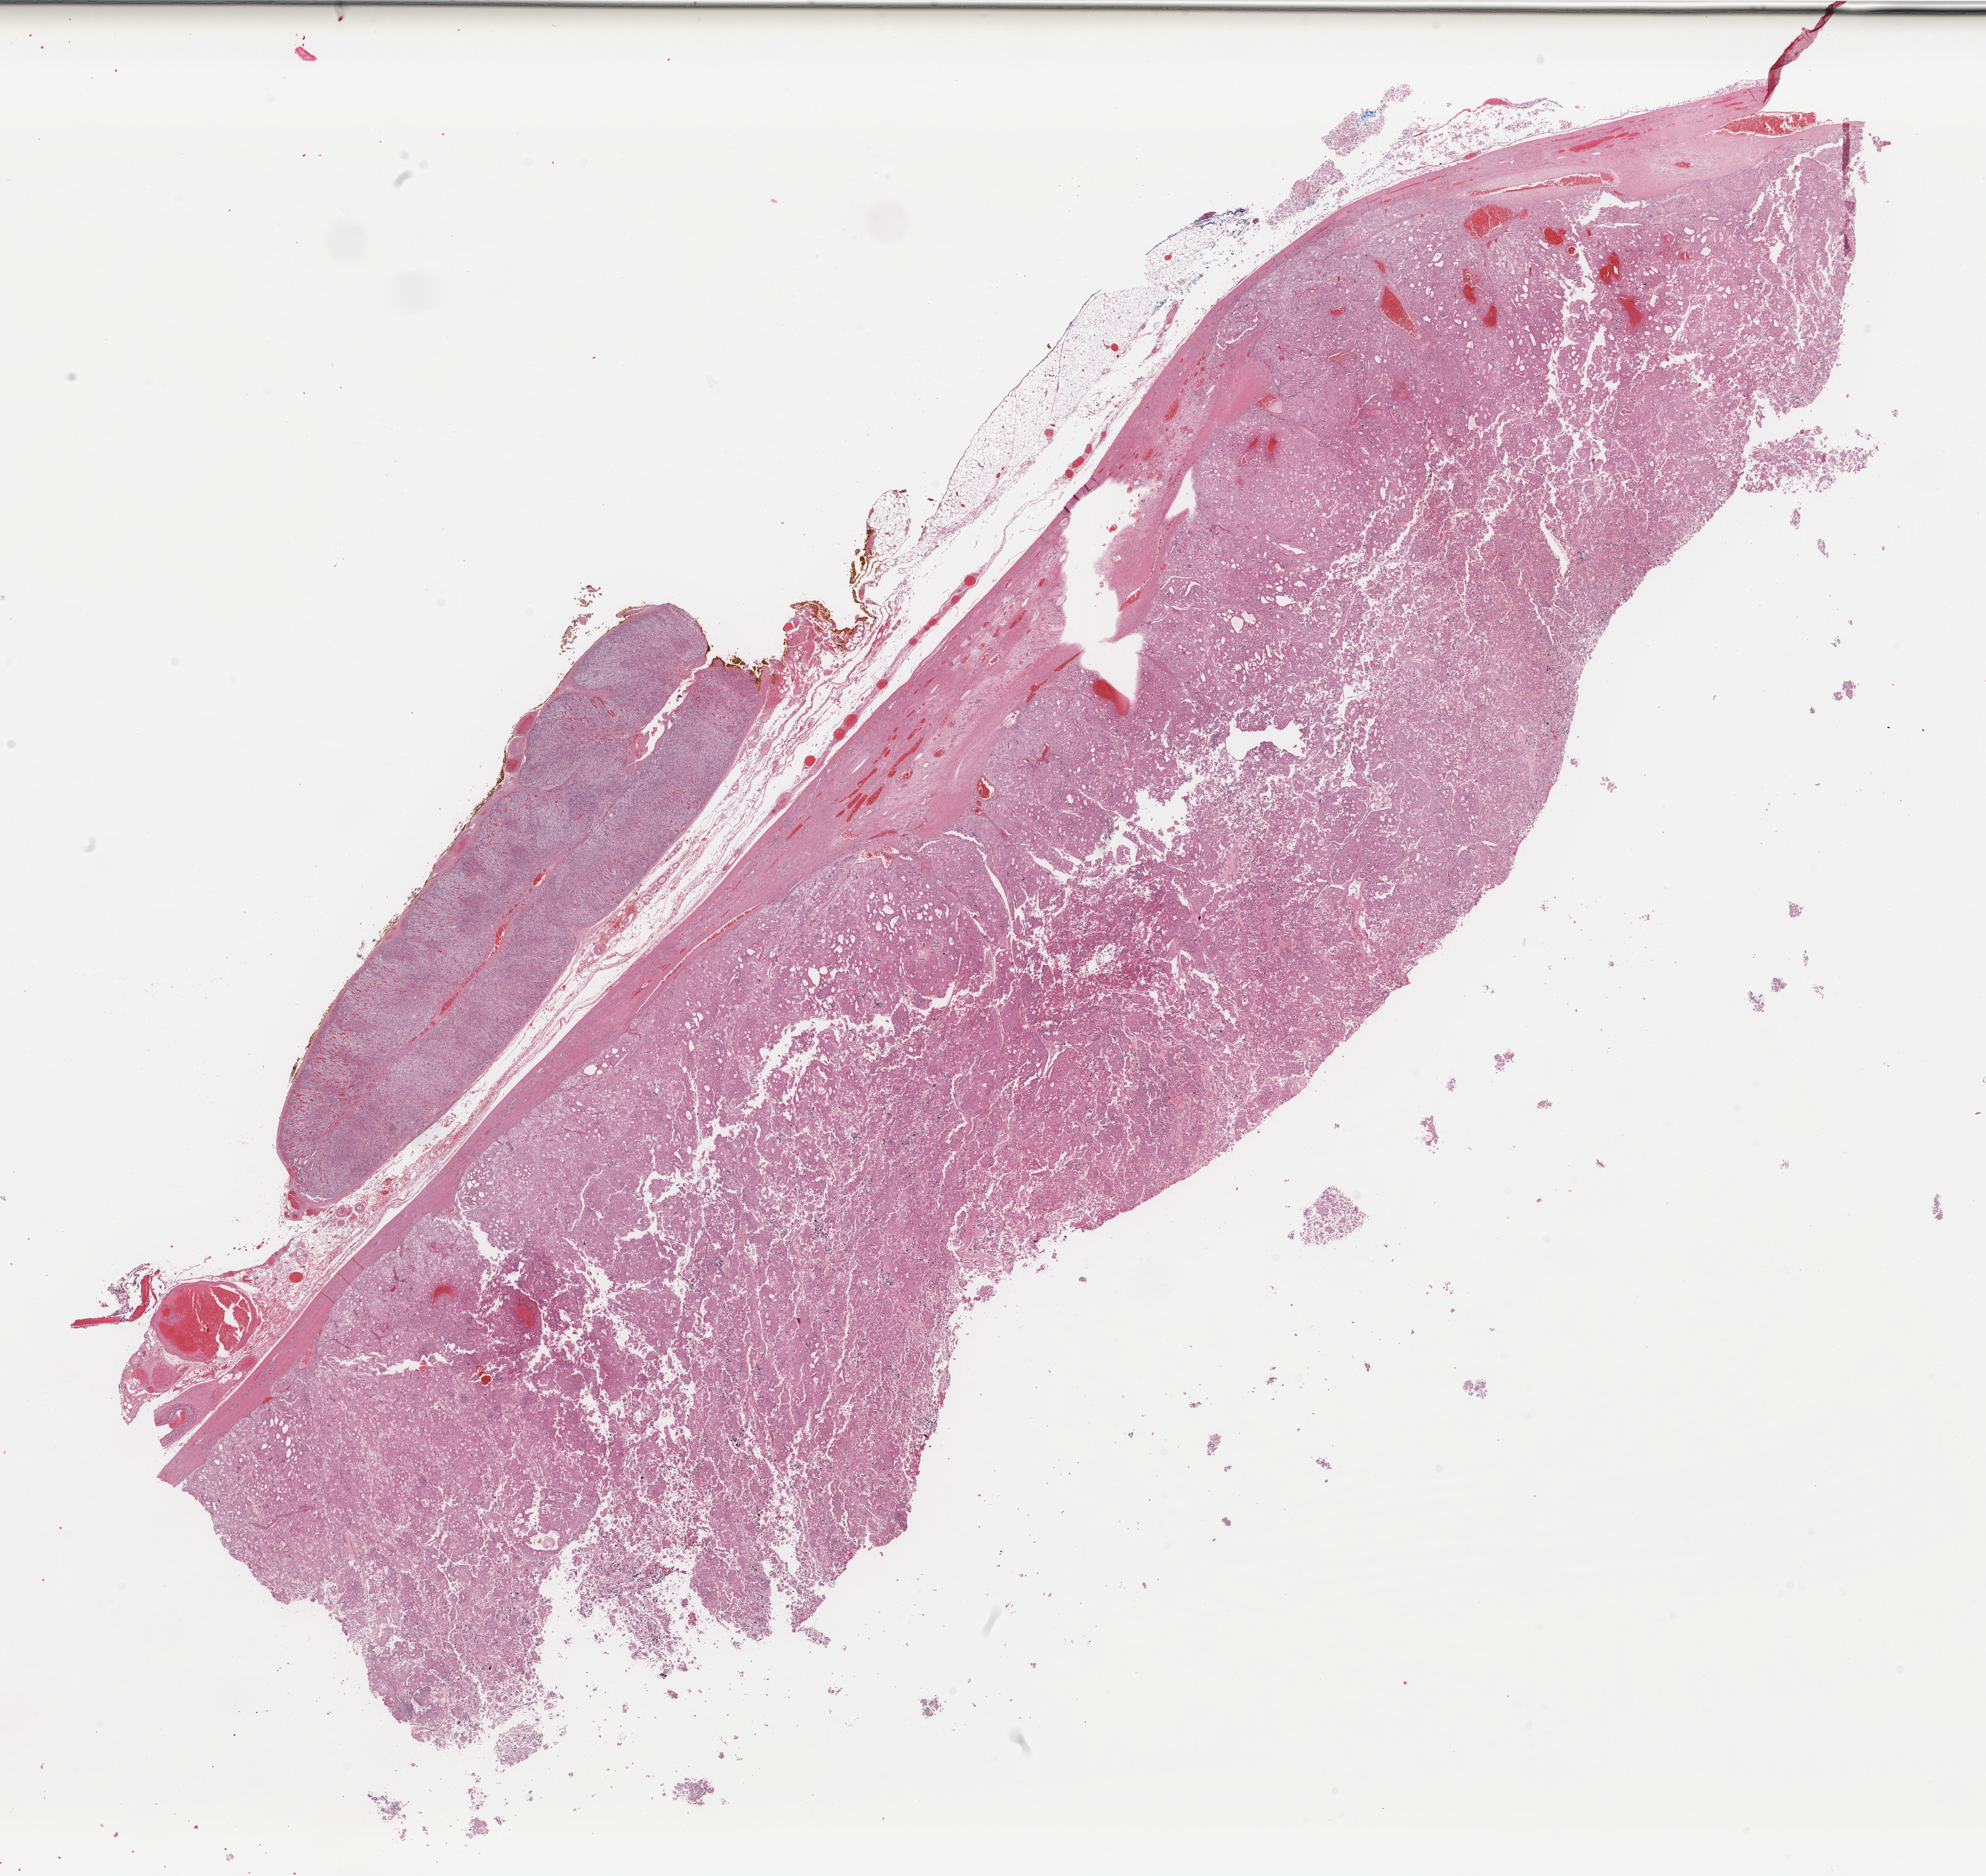
Digitized H&E-stained tissue section (whole slide) — shown as a low-resolution overview of the whole scanned area (about 25.2 x 23.8 mm), FFPE section, solid tissue normal (non-tumour tissue) sample from the kidney. Female, age 52 years at initial diagnosis. Pathologist review of this section (percent, as recorded): tumour cells 0%, tumour nuclei 0%, normal cells 70%, stromal cells 30%, necrosis 0%. Infiltration values recorded for this section: lymphocyte infiltration 3%, monocyte infiltration 1%, neutrophil infiltration 1%.
• this section: solid tissue normal (non-tumour) sample from the same patient
• patient diagnosis: Renal cell carcinoma, chromophobe type